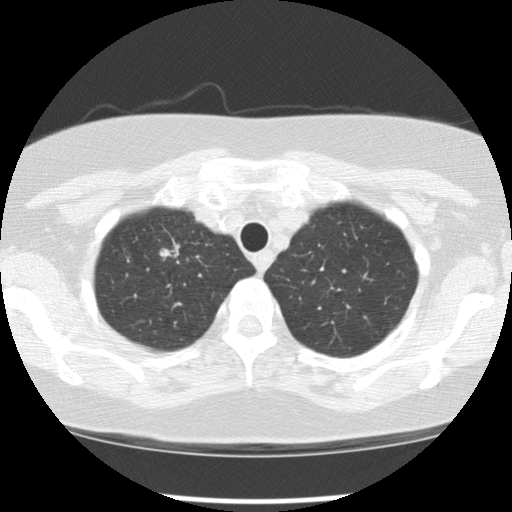
Axial slice from a low-dose chest CT screening exam, first (baseline) screen, lung window (W 1500 / L -600 HU), 2.5 mm slice thickness, 512 × 512 image matrix. Female, age 65 years at enrolment. Current smoker at enrolment.
- Expert reader's lesion annotation, box from (x=148, y=232) to (x=196, y=280) px.
- The screening reader recorded 2 non-calcified nodules or masses ≥4 mm on this exam (right upper lobe, right upper lobe); which of them this box marks is not recorded.